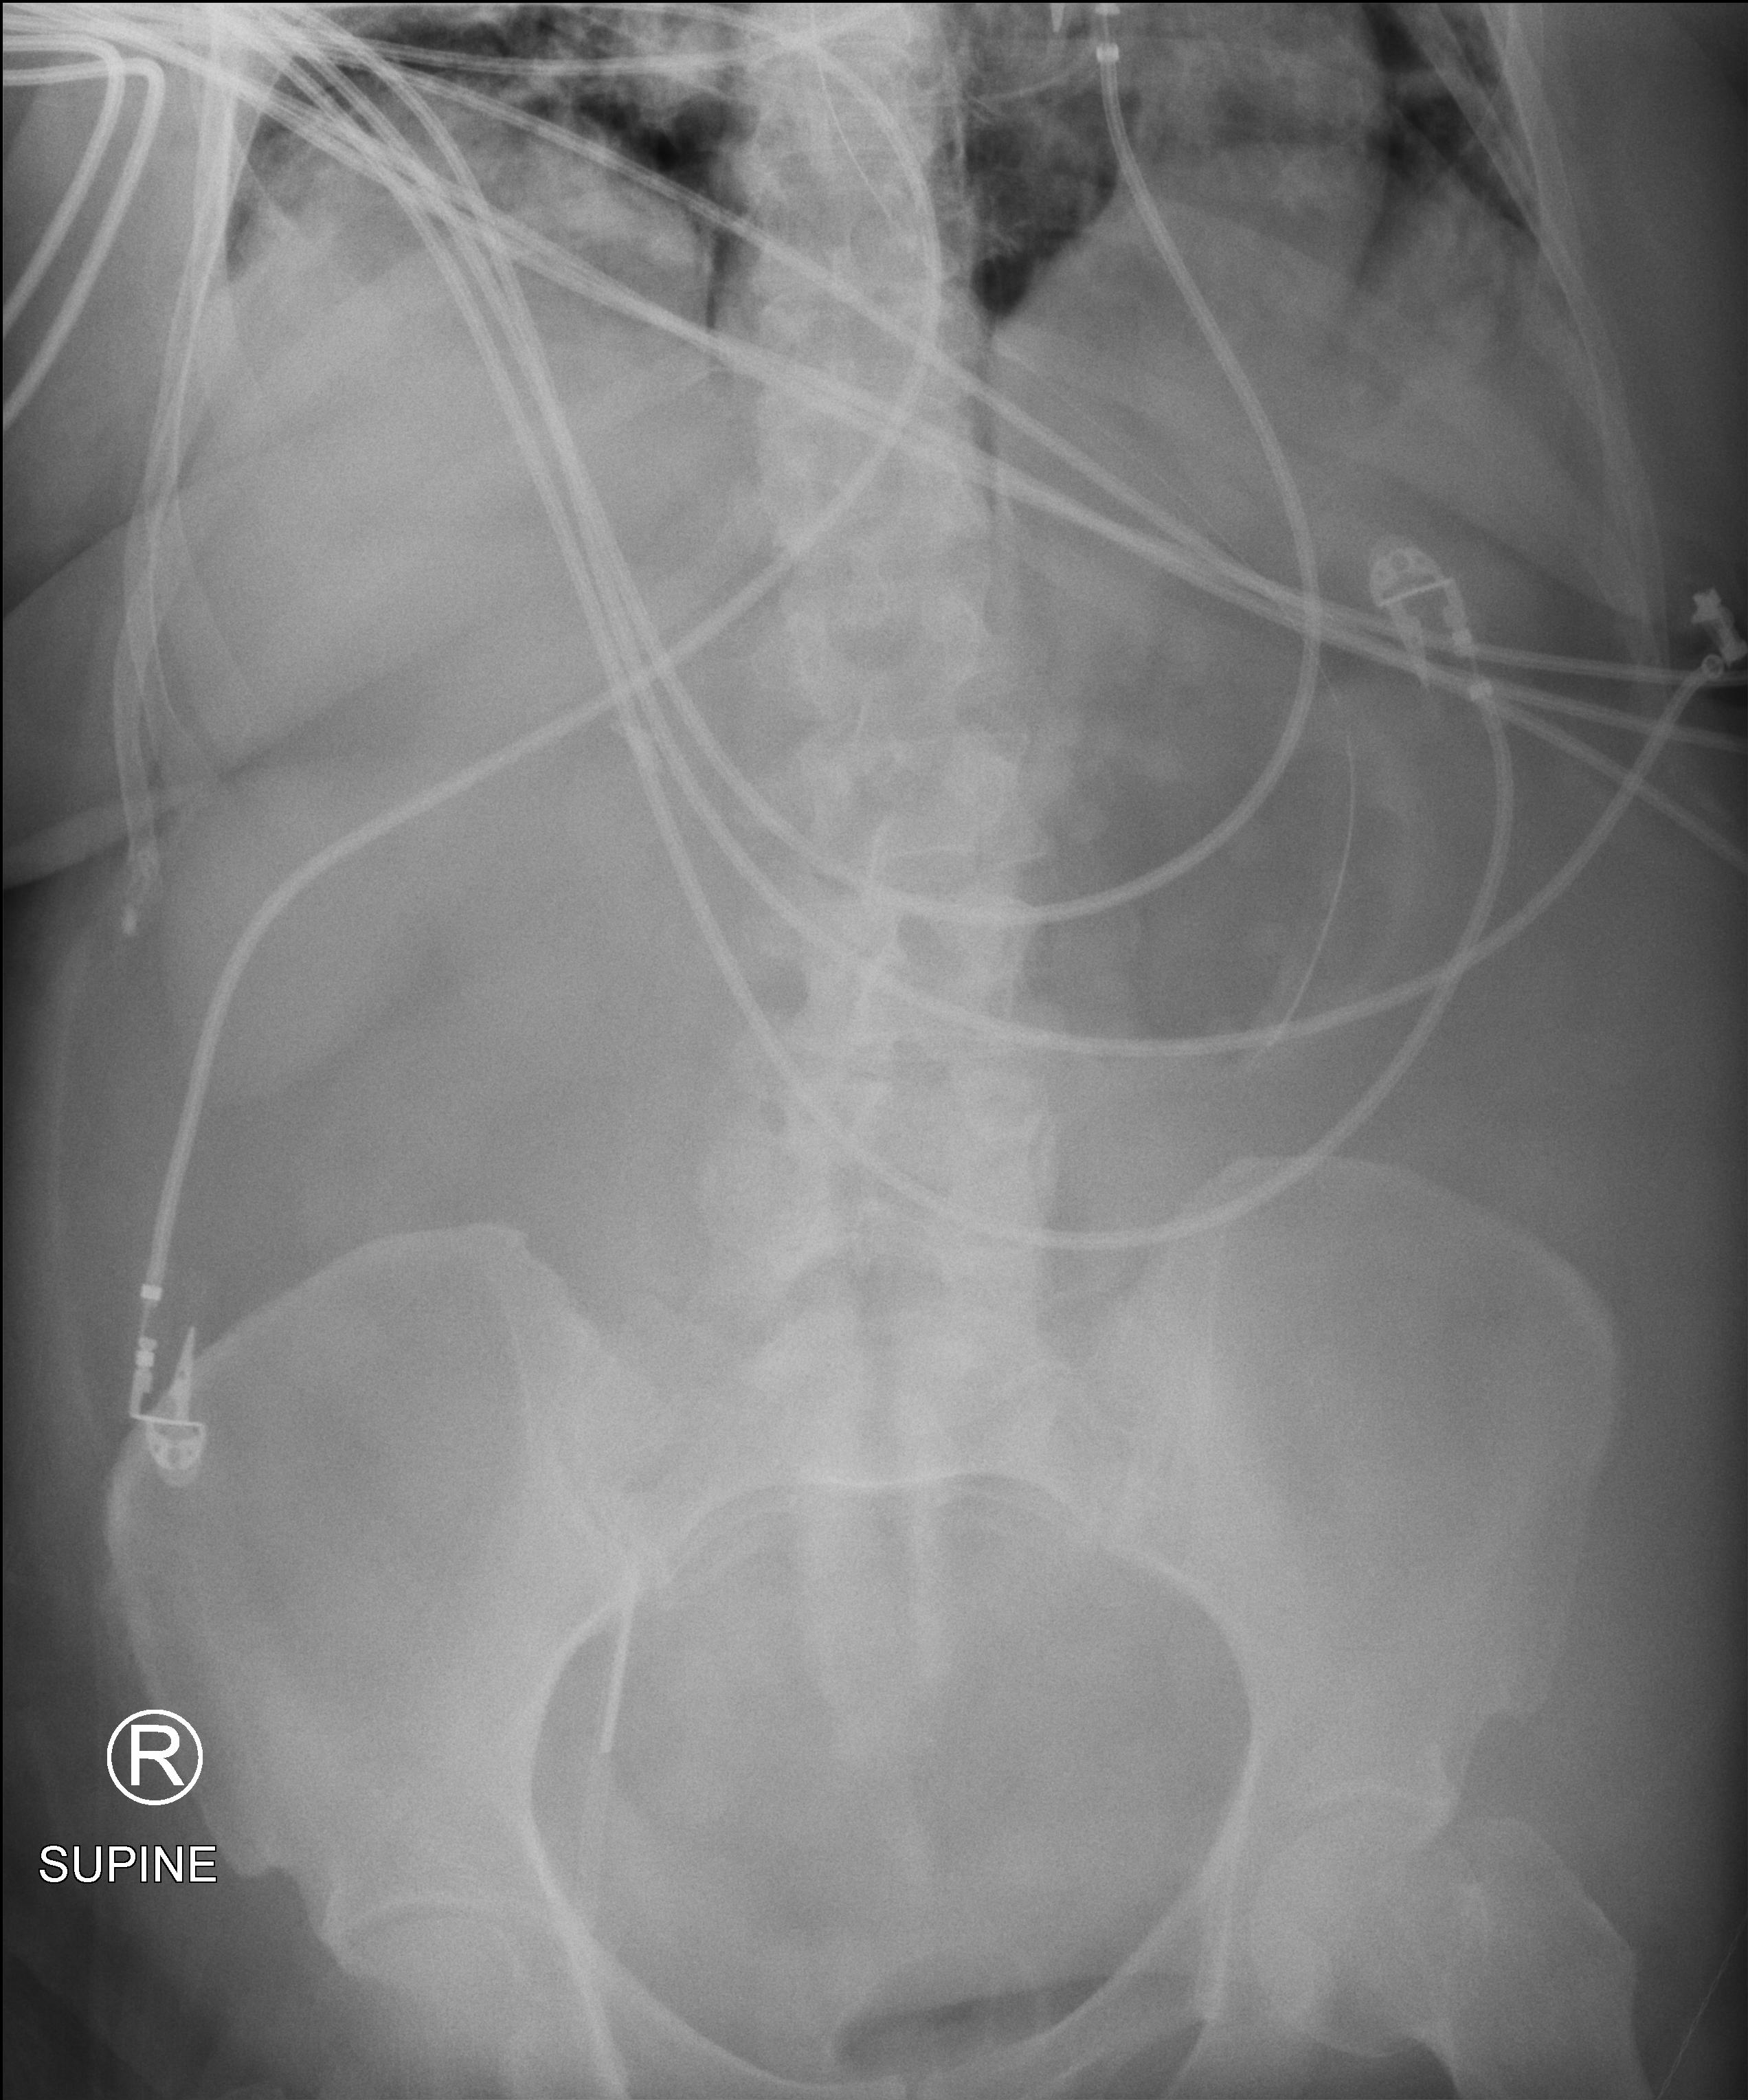
Portable abdomen radiograph, anteroposterior (AP) projection. Patient hospitalised with COVID-19; female, aged 60–74 years.
From the hospital-stay record, not from the radiograph (when in the stay this image was taken is not recorded):
- length of hospital stay: 45 days
- smoking status (admission record): never
- mechanically ventilated during this hospital stay: yes